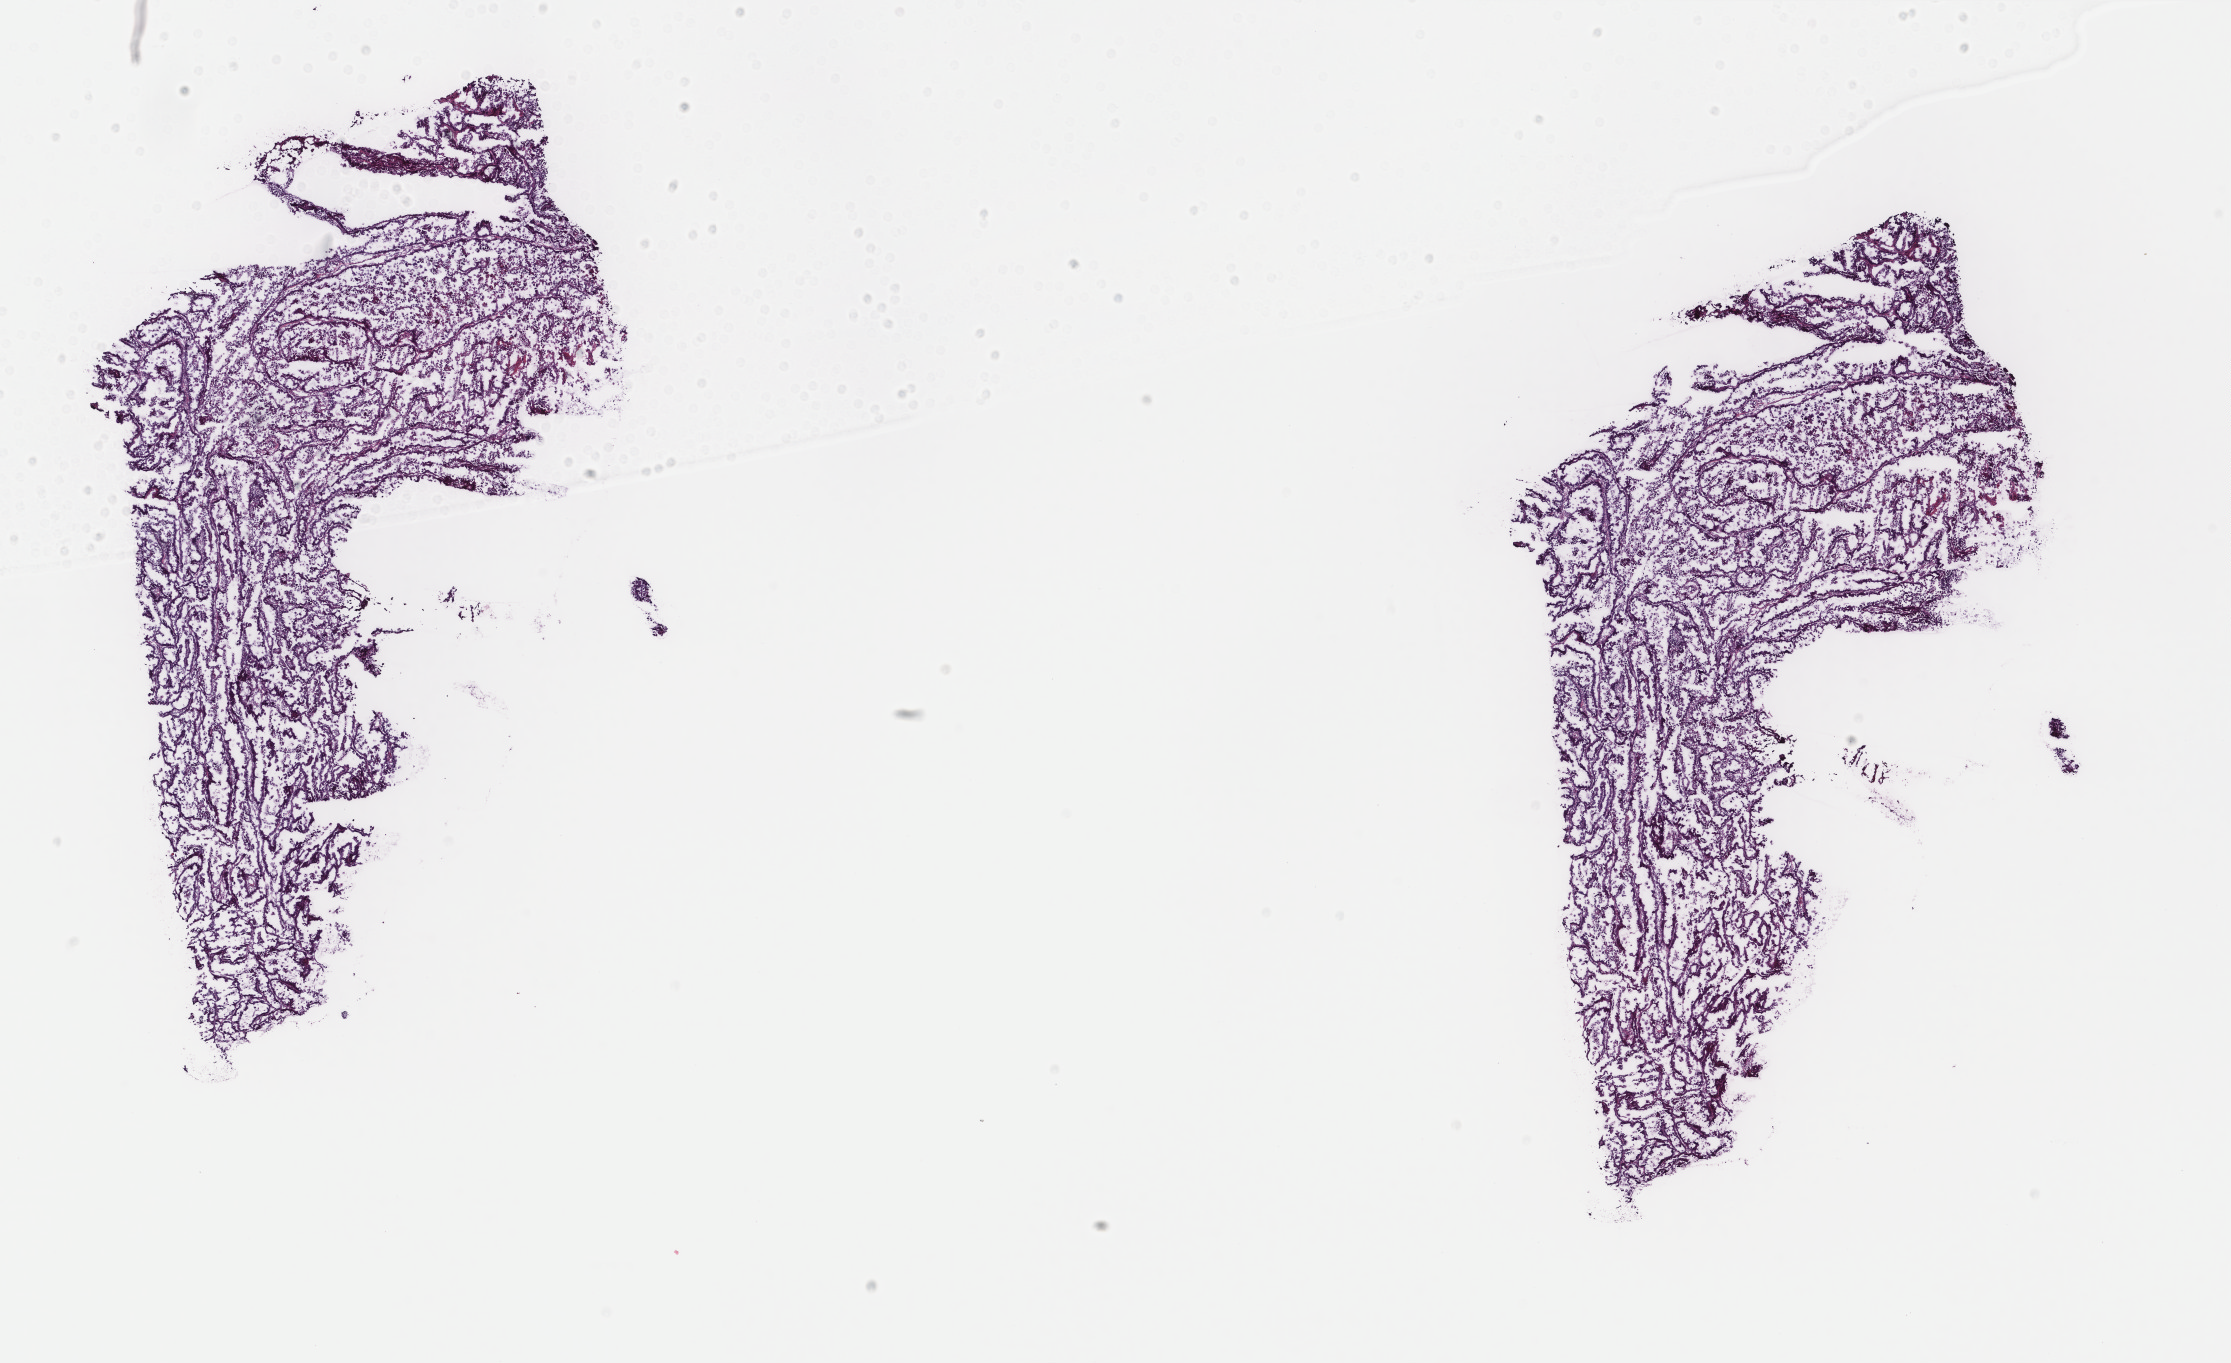
Digitized H&E-stained tissue section (whole slide), whole scanned area (about 17.7 x 10.8 mm) shown as a low-resolution overview. Frozen section. Uterus, primary tumour sample. Female patient; age at initial diagnosis 66 years. Histologic grade: G3 (poorly differentiated). Pathologist review of this section (percent, as recorded): tumour cells 96%, tumour nuclei 98%, normal cells 0%, stromal cells 2%, necrosis 2%. Infiltration values recorded for this section: lymphocyte infiltration 5%, monocyte infiltration 5%, neutrophil infiltration 5%.
* diagnosis: Serous cystadenocarcinoma, NOS (endometrium)
* FIGO stage: IB